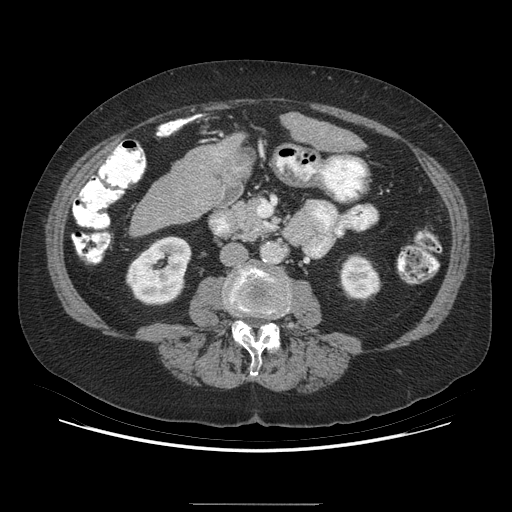
Contrast-enhanced abdominal CT (liver protocol), one axial slice. Slice 127 of 192 in the series (ordered by position). Soft-tissue window (W 400 / L 40 HU). 512 × 512 image matrix, field of view 400 × 400 mm. Case-level facts recorded for this patient, not image findings: diagnosis: hepatocellular carcinoma (patient treated with transarterial chemoembolisation; whether this scan precedes or follows treatment is not stated here); TNM stage (as recorded): Stage-I; Child-Pugh class: A.
Annotated regions visible in this slice (semi-automatically segmented with operator editing):
- liver parenchyma outside the tumour (the mass and vessels are separate outlines, so this box may not span the whole liver): bounding box <292,124,360,148> (left, top, right, bottom; pixels)
- mass: <218,156,245,184>